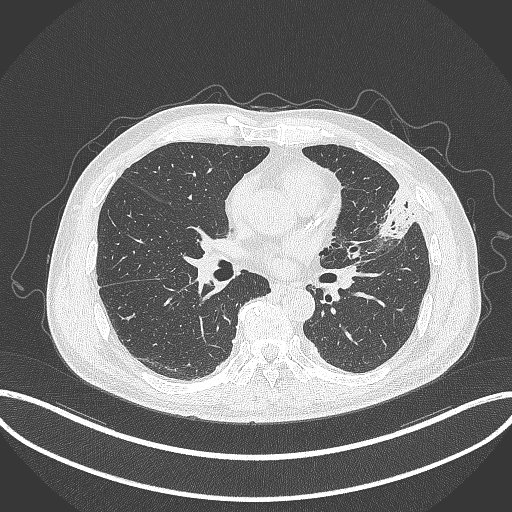
Chest CT, one axial slice. Position 163 of 382 along the scan axis. 120 kVp. Lung window (W 1500 / L -600 HU). 1 mm slice thickness. 512 × 512 image matrix, field of view 415 × 415 mm. Patient: male, 64 years. From the clinical record (not read from this slice): clinical TNM (as recorded): T4 N1 M0.
Outlined on this slice (rectangle marked by the reading radiologist):
- lung tumour (recorded histology: adenocarcinoma): bounding box [x1, y1, x2, y2] px = [373, 182, 421, 242]